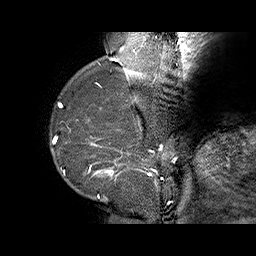
Breast MRI (dynamic contrast-enhanced), one sagittal slice; dynamic contrast-enhanced series, time point 2 of 6 at this slice position (early post-contrast); 1.5 T; TE 4.5 ms, TR 32.4 ms; 256 × 256 image matrix, field of view 180 × 180 mm. Female patient. From the clinical record (not read from this slice): setting: breast cancer imaged before/during neoadjuvant chemotherapy; receptor status: HR-positive, HER2-negative.
Outlined on this slice (semi-automatic segmentation, software-assisted and operator-edited):
- analysis volume of interest (the breast-tissue region the enhancement analysis was run in; not a lesion): bounding box [x1, y1, x2, y2] px = [71, 128, 159, 202]
- tumour enhancement mask (voxels above the 100 % enhancement threshold inside the analysis volume of interest): [88, 137, 158, 197]